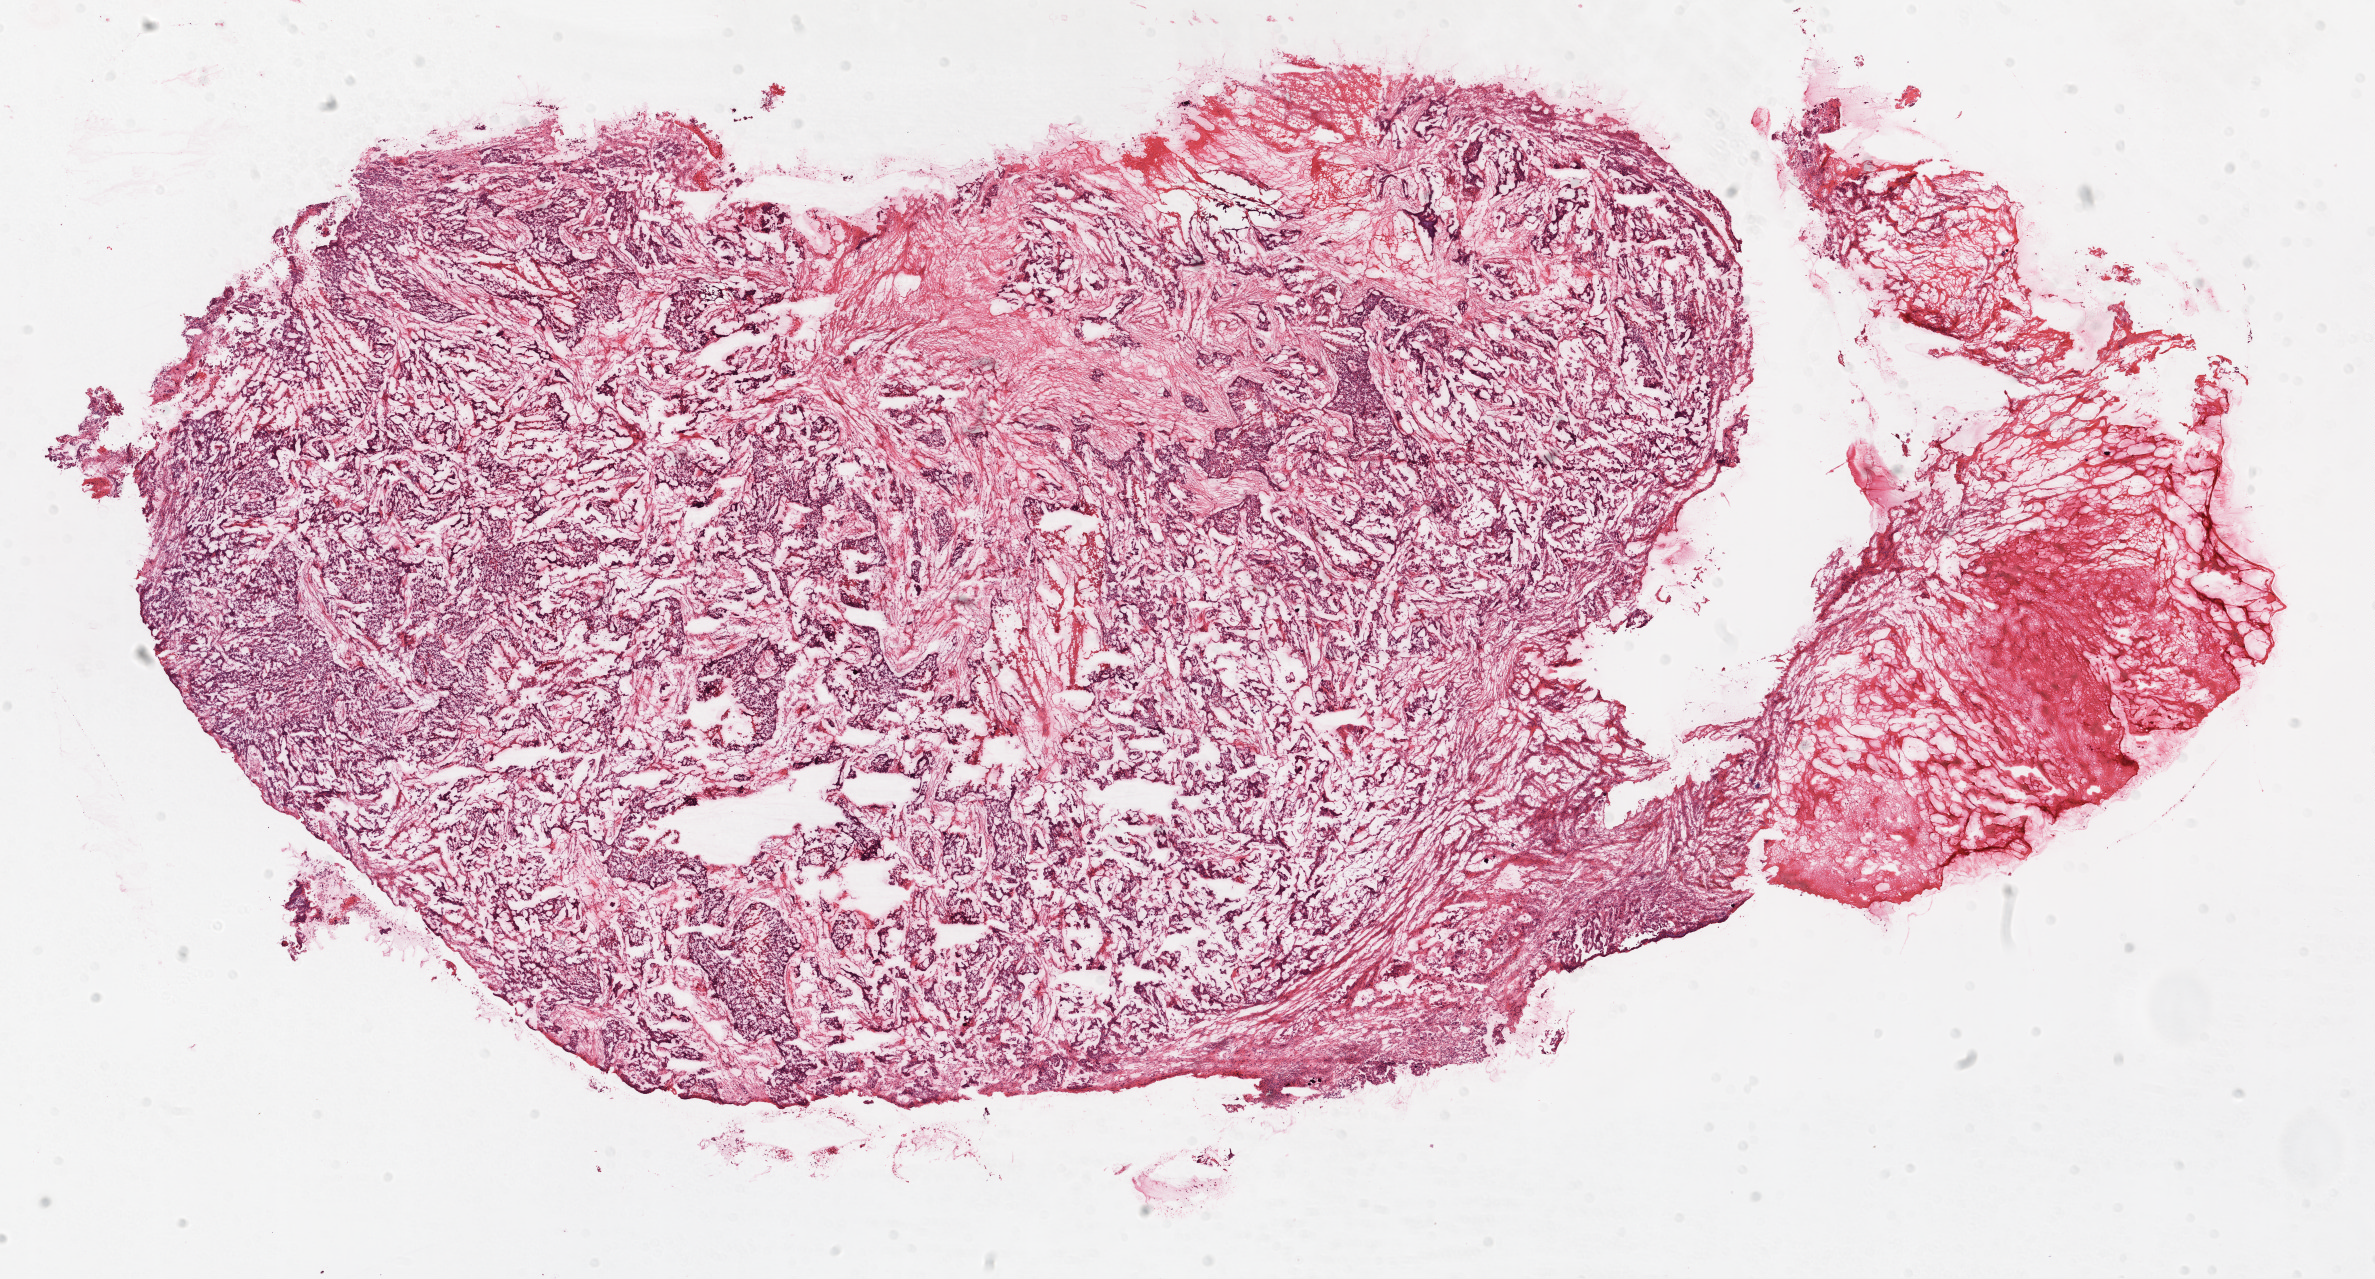
H&E whole-slide image, whole scanned area (about 19.1 x 10.3 mm) shown as a low-resolution overview; frozen section; sample: primary tumour, ovary. Female patient; age at initial diagnosis 53 years. Histologic grade: G3 (poorly differentiated). Composition of this section per pathologist review: tumour cells 70%, tumour nuclei 70%, normal cells 0%, stromal cells 30%, necrosis 0%.
FIGO stage: IIC. Pathologic diagnosis: Serous cystadenocarcinoma, NOS.